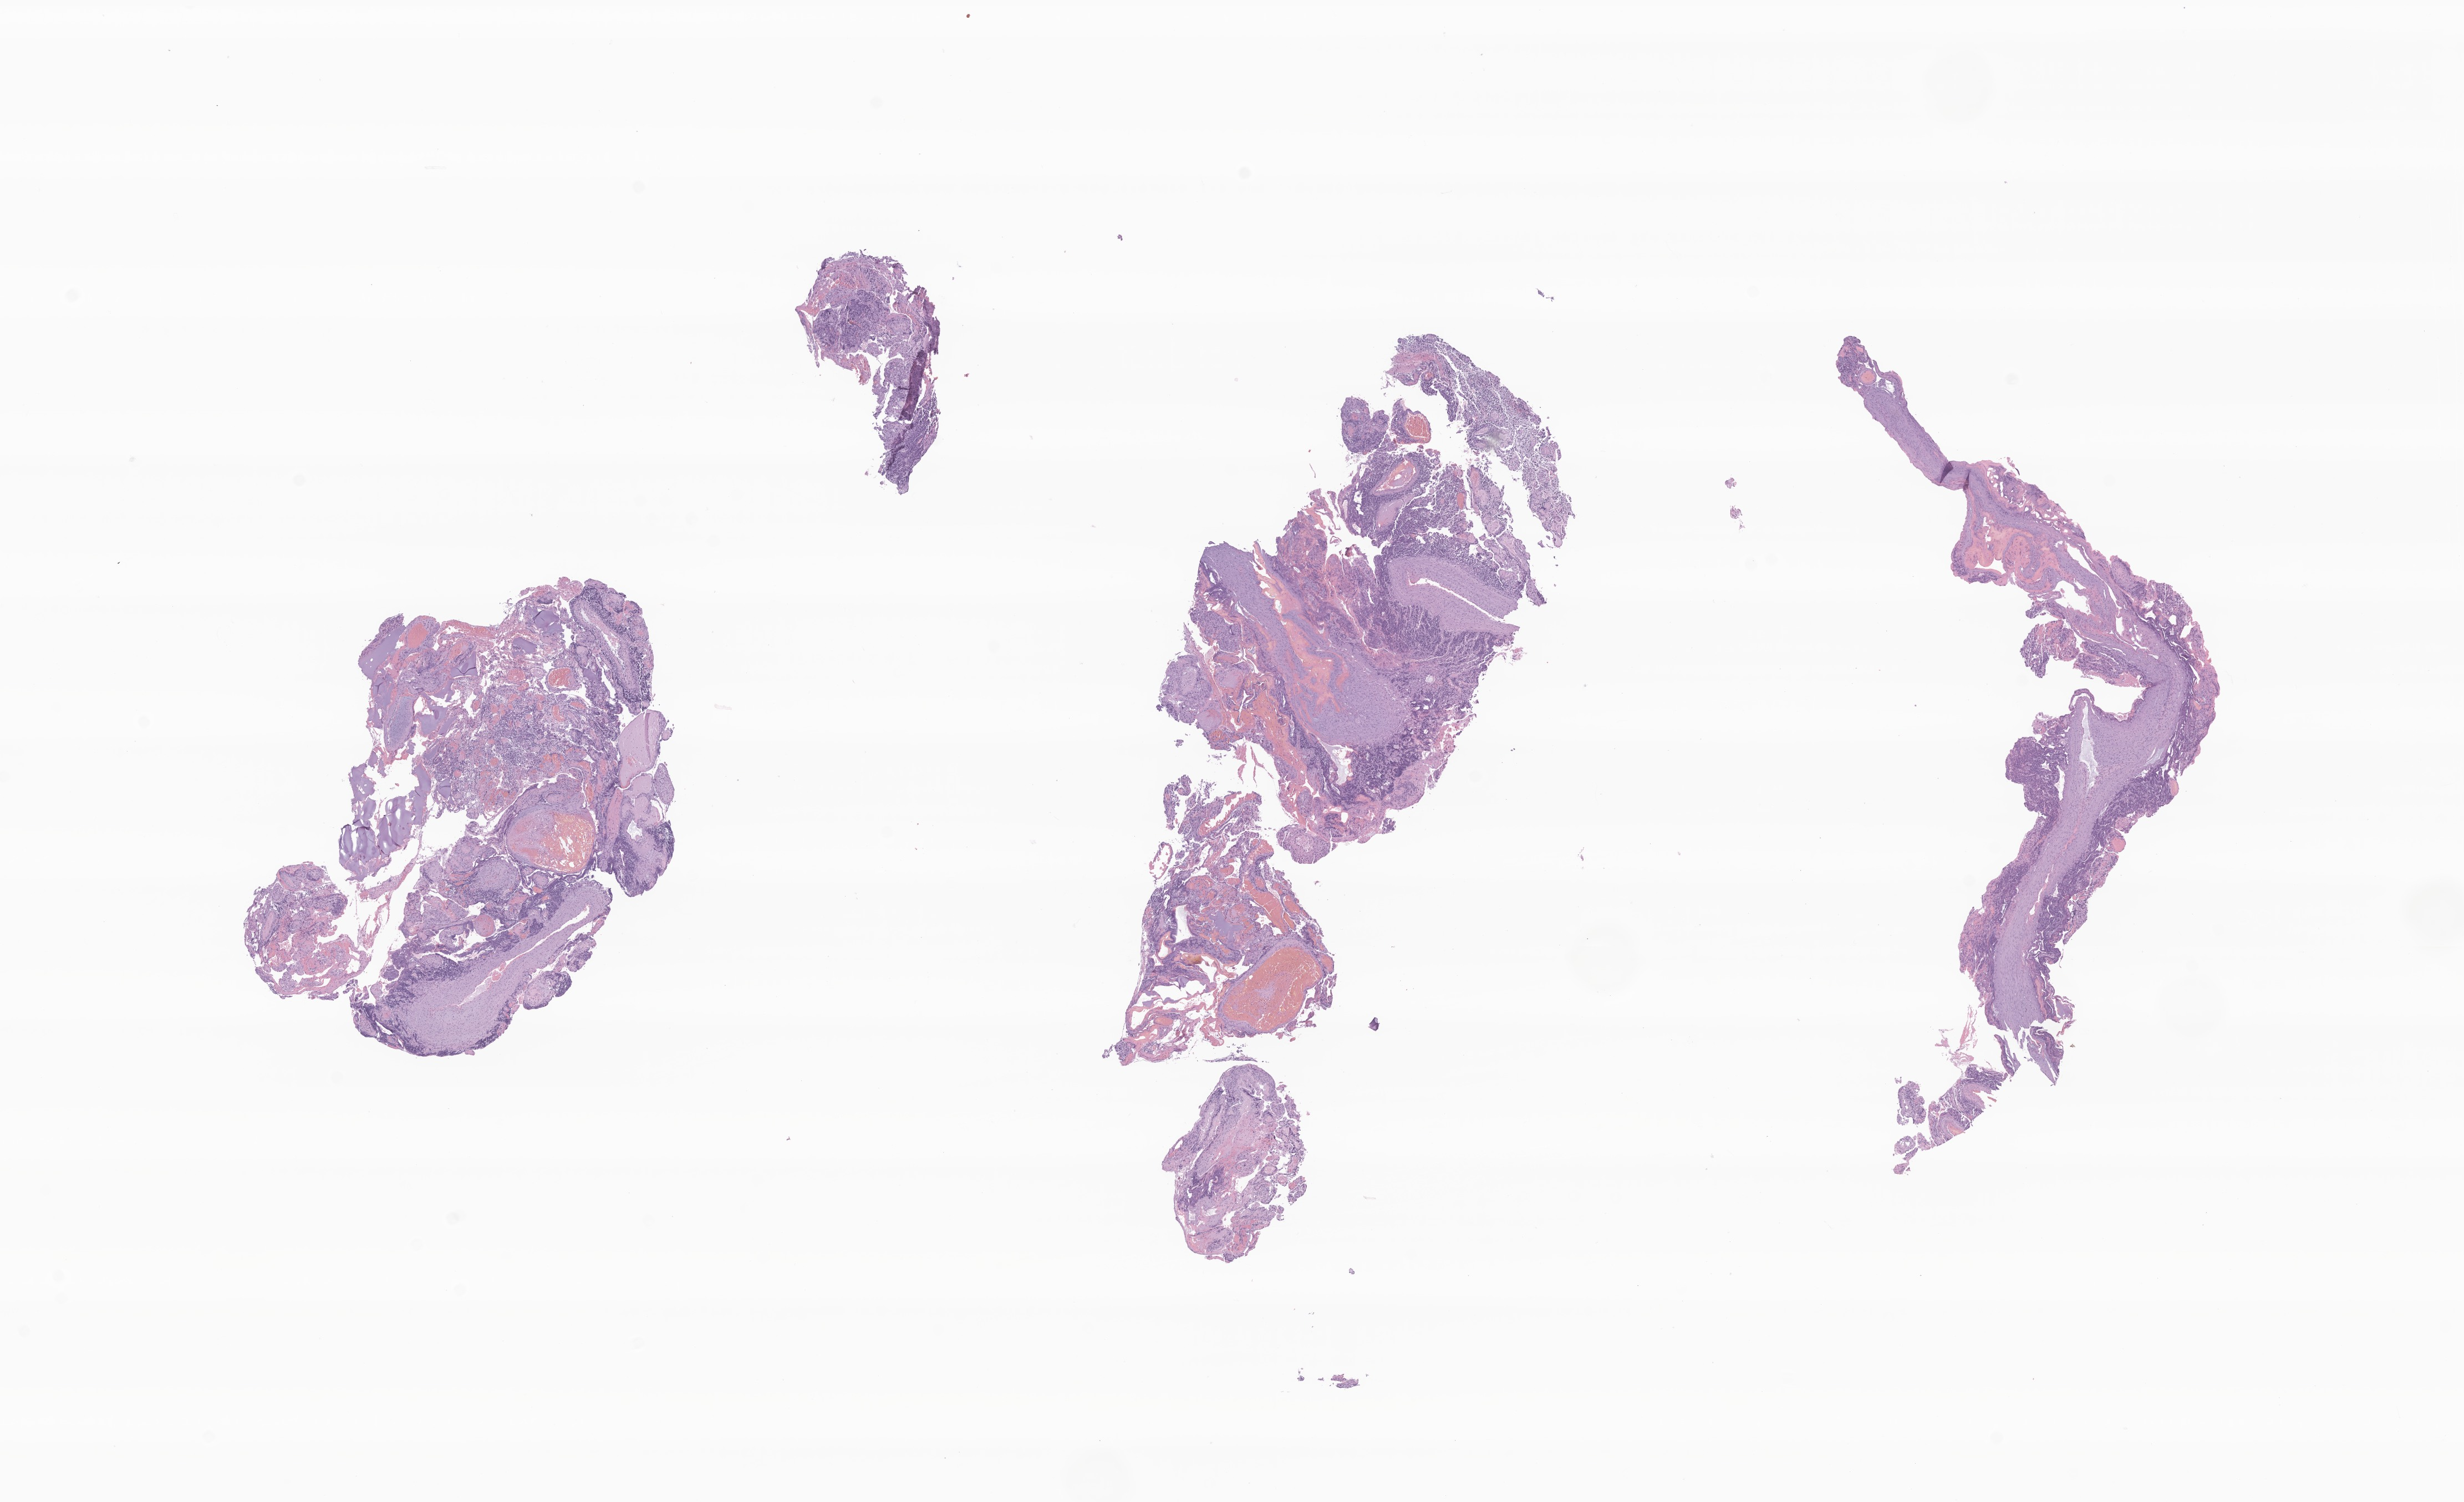
Digitized H&E-stained section of tumor tissue from the cerebellum — whole scanned area (about 18.7 x 11.4 mm) shown as a low-resolution overview, formalin-fixed, paraffin-embedded (FFPE) tissue. Male patient, age 810 days (about 2.2 years).
• diagnosis: Medulloblastoma, NOS